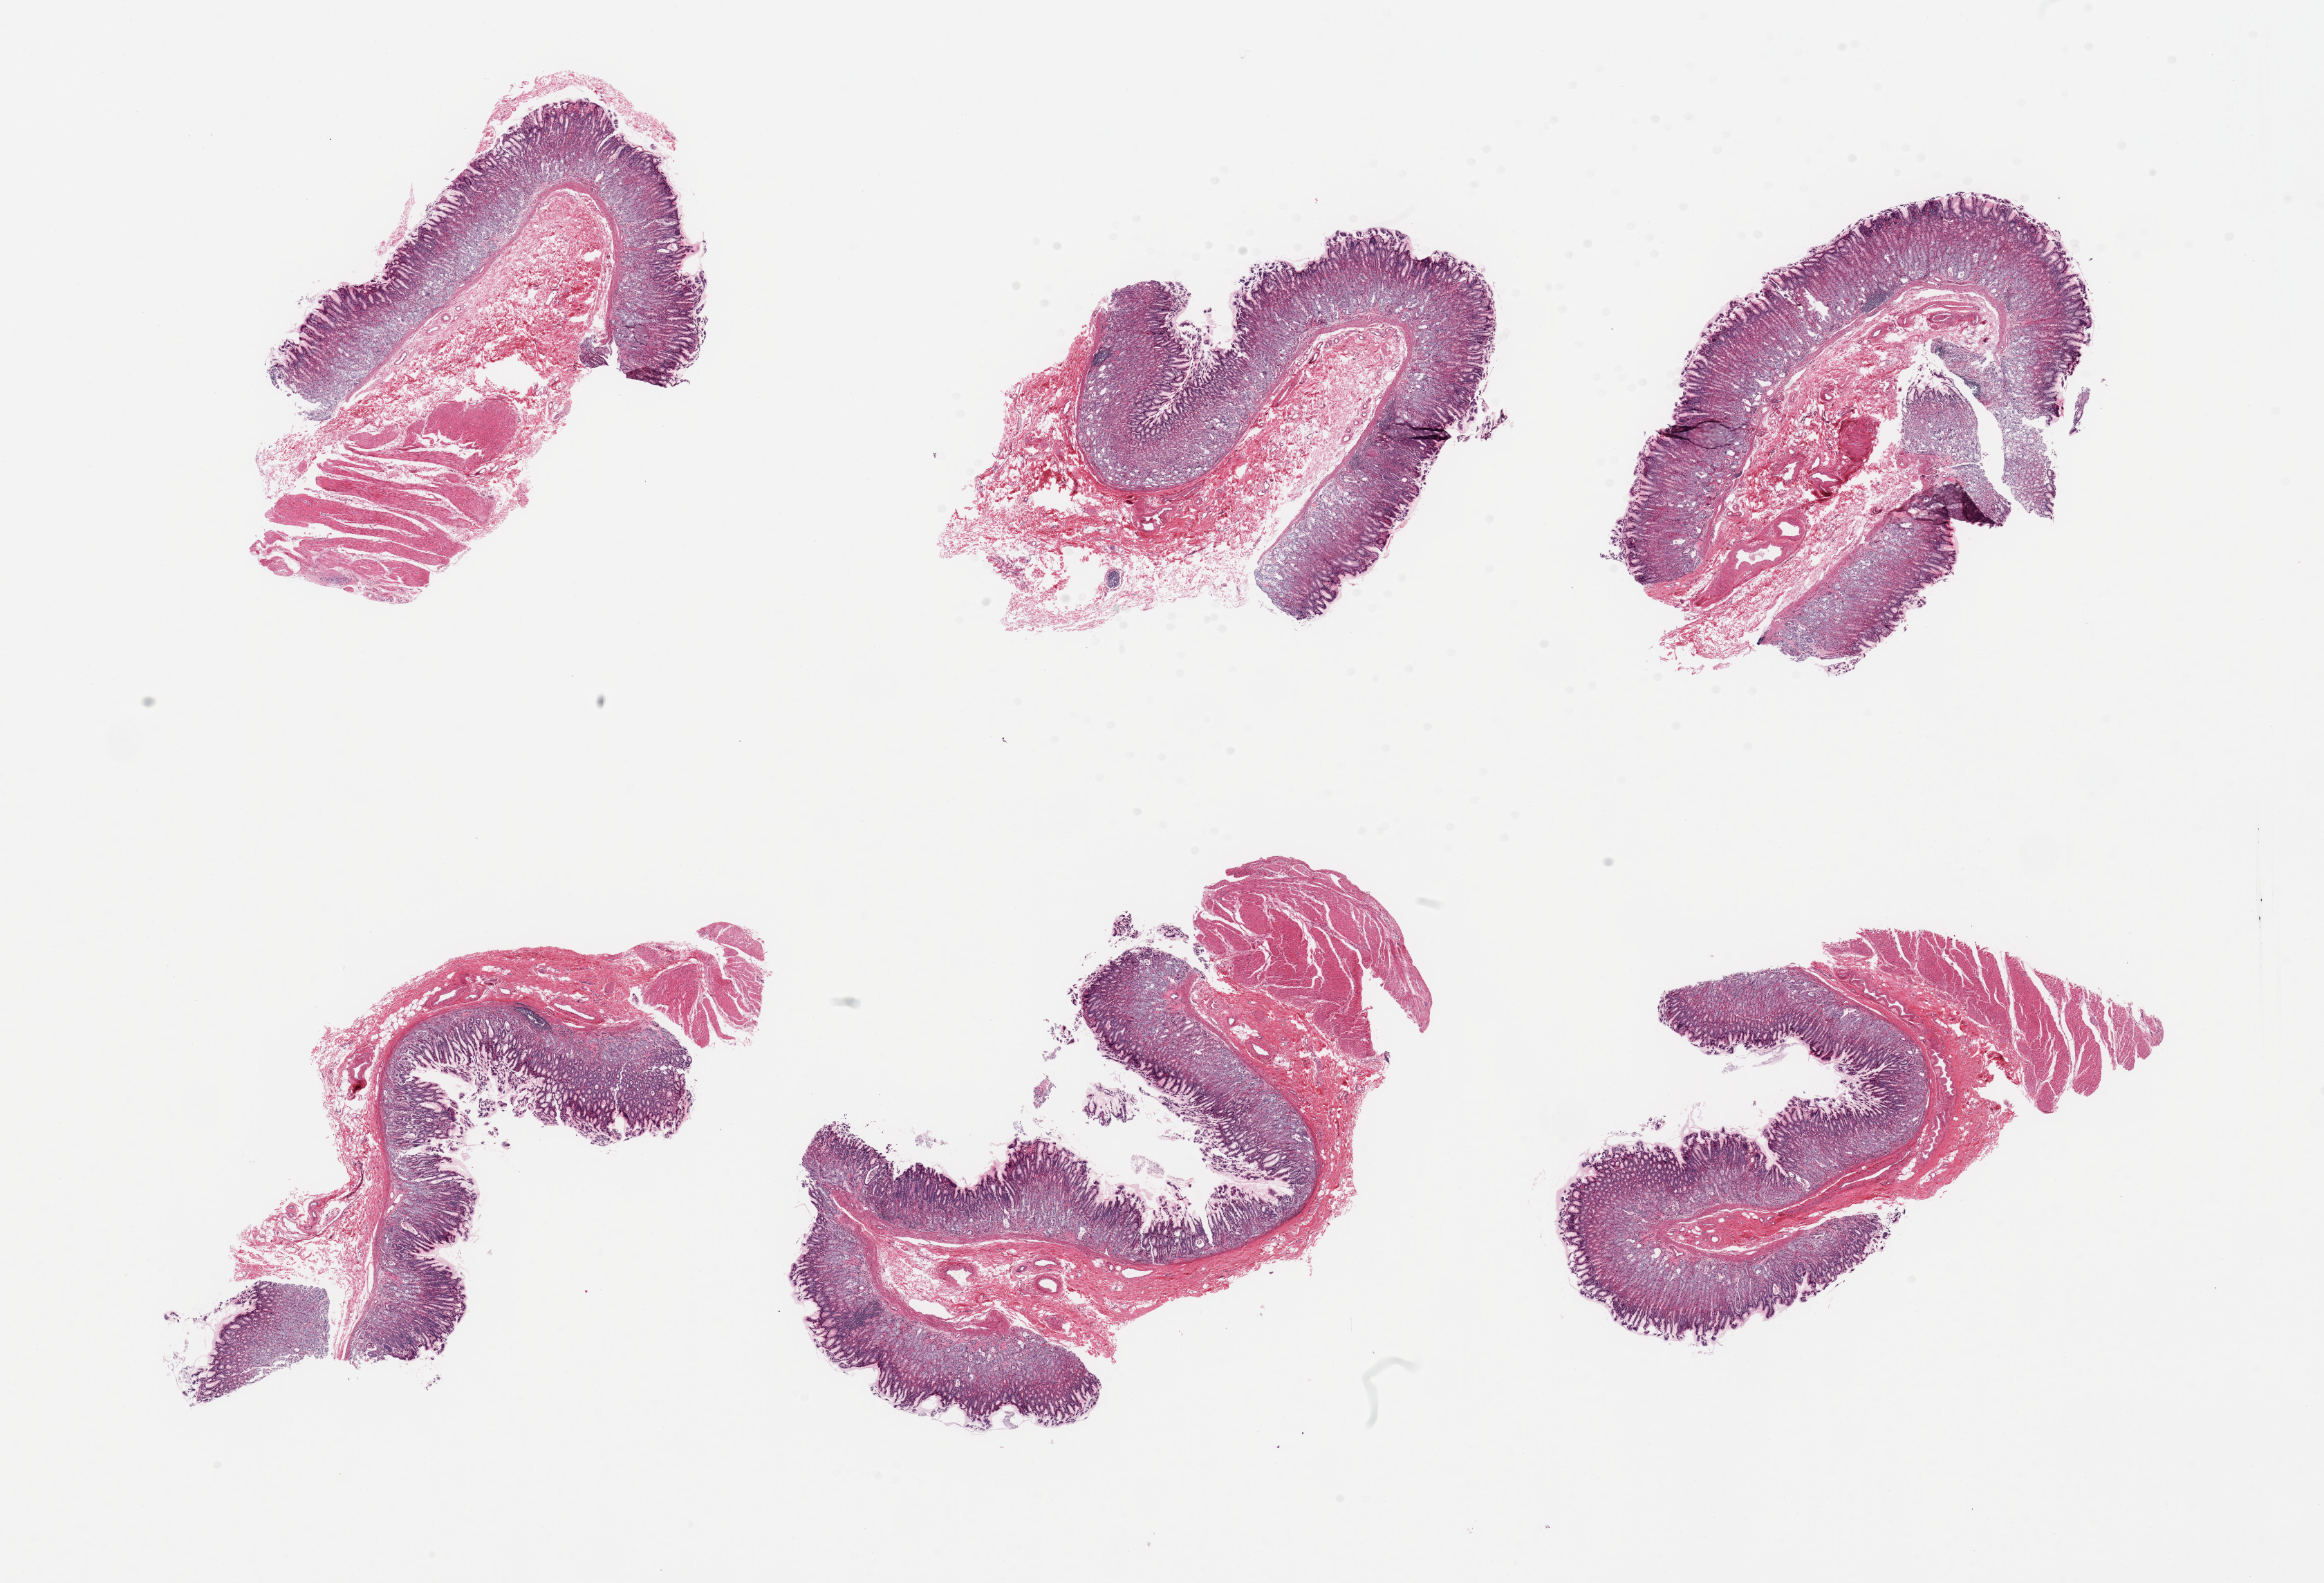
Digitized H&E-stained section, a low-resolution overview of the entire scanned area, about 26.6 x 18.1 mm (acquisition: 20x scan), PAXgene-fixed paraffin-embedded (PFPE) section, section of stomach (target tissue), donor tissue sample. Male donor.
• pathologist's review note for this sample: 6 pieces, mucosa up to ~1mm, ~40-50% thickness